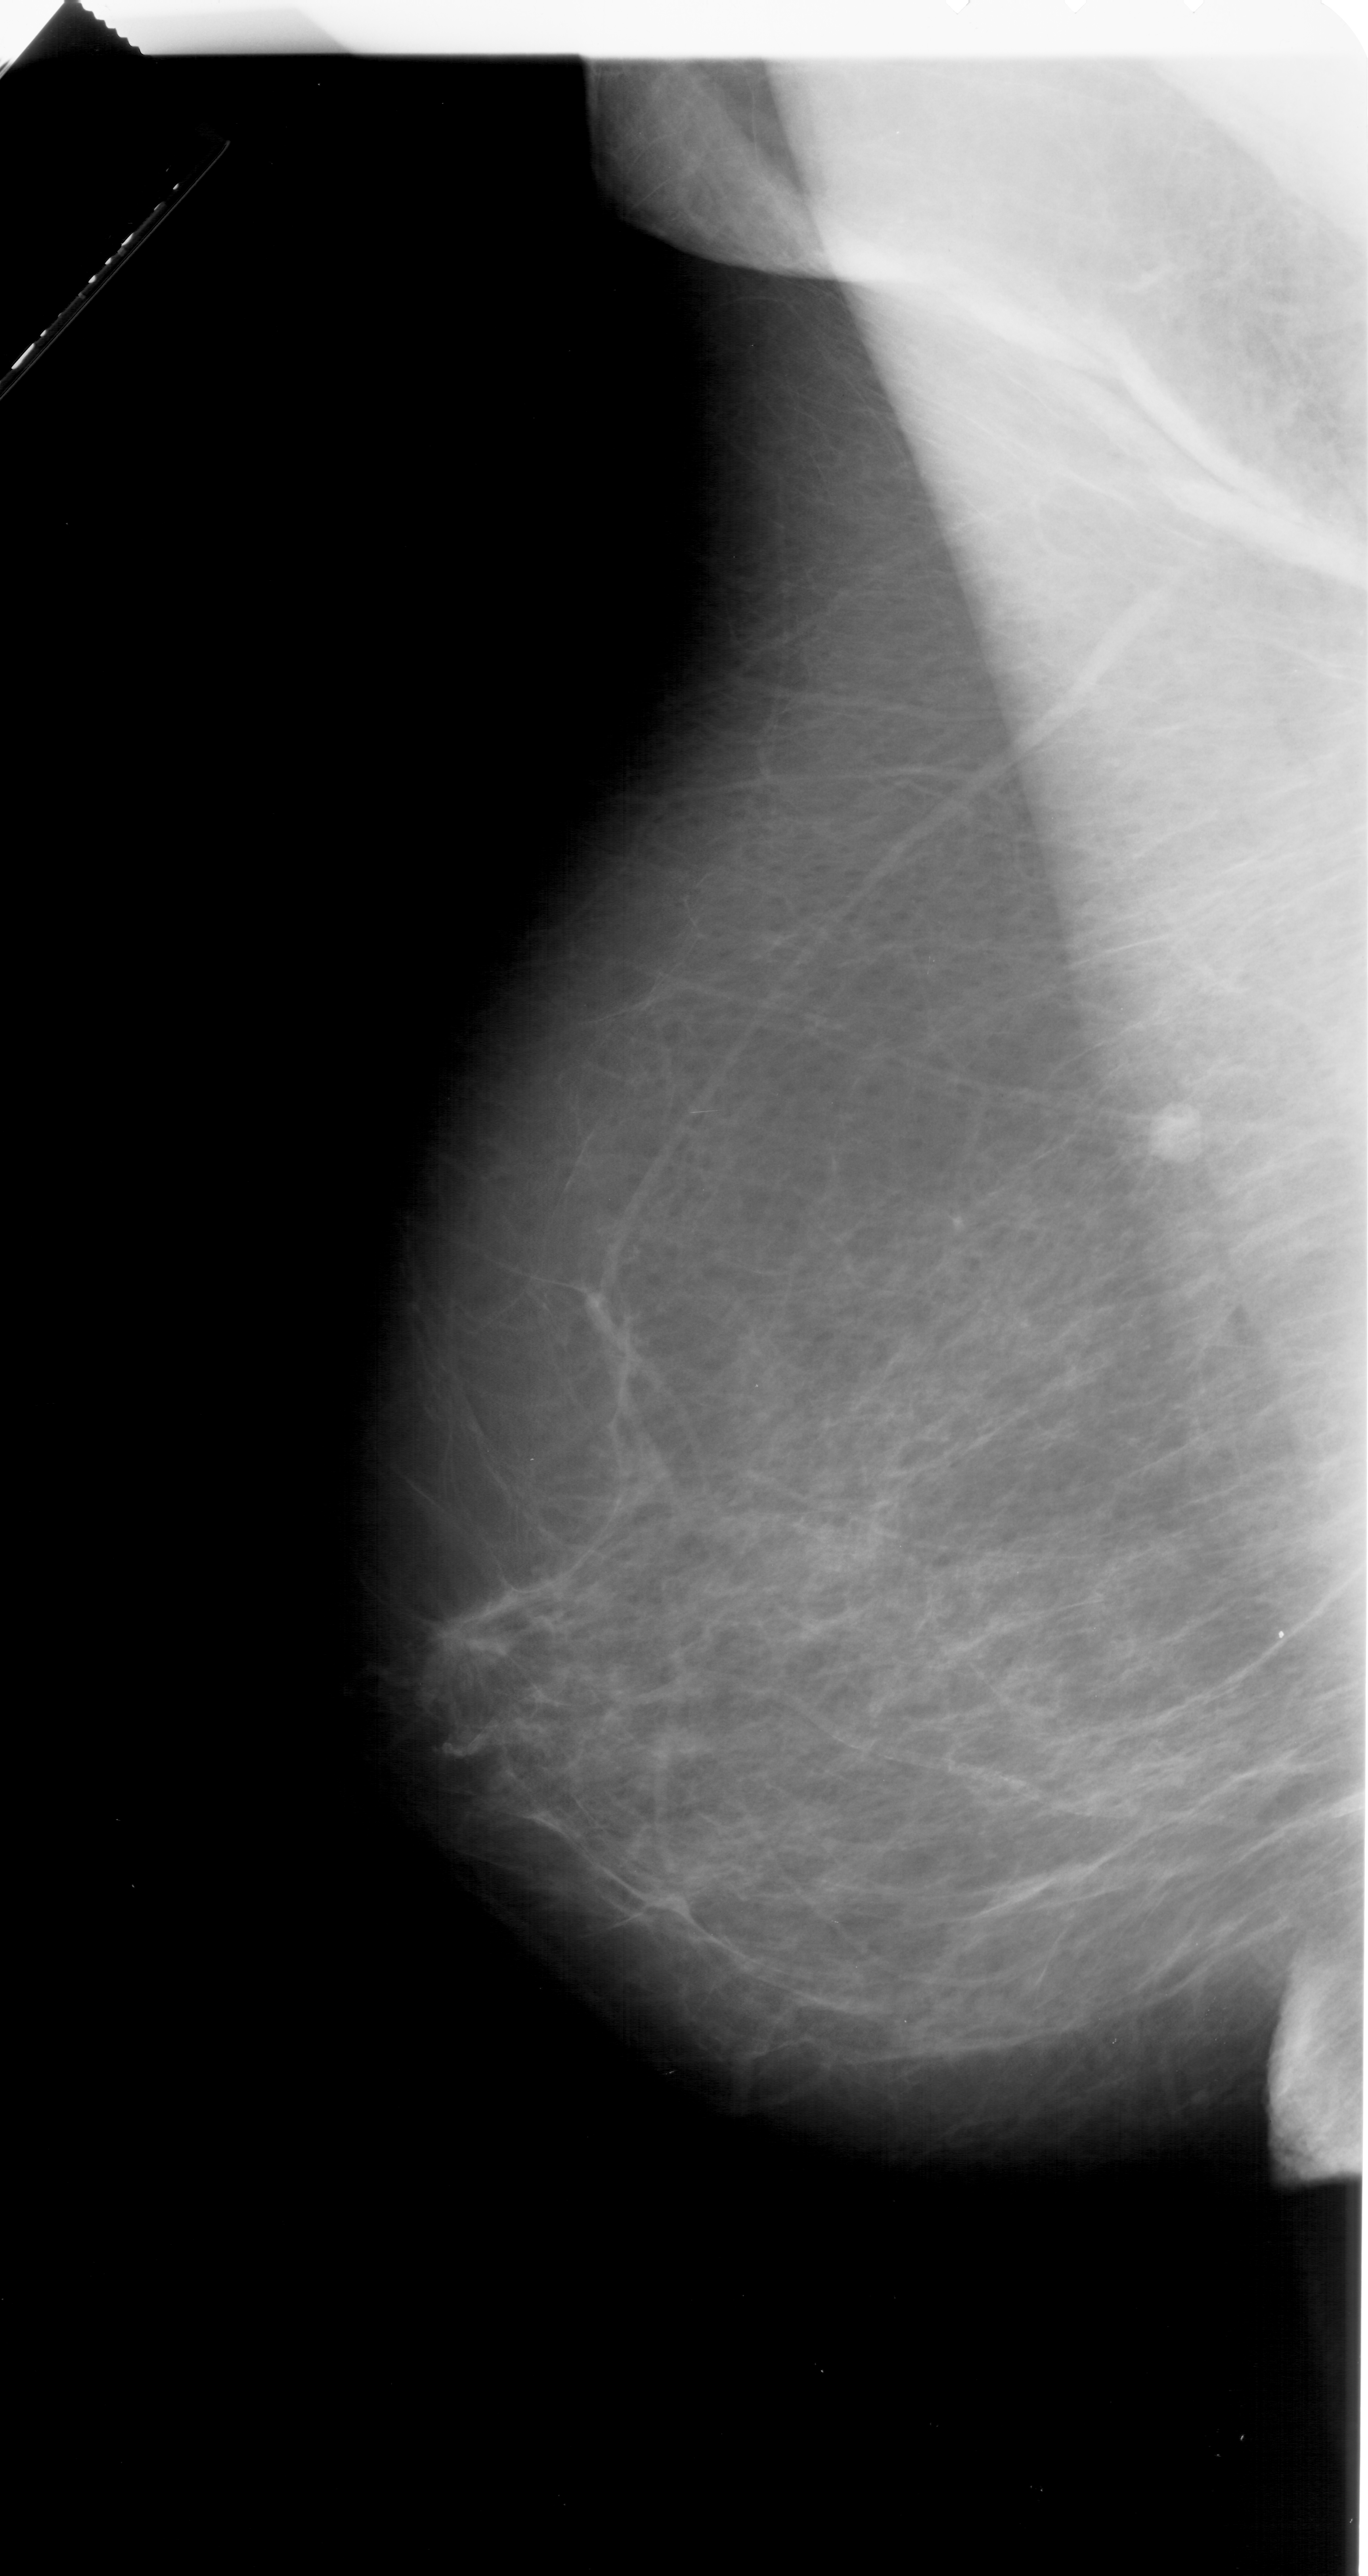
Mammogram (digitized film). Left breast. Mediolateral oblique (MLO) view. 1368 × 2576 image matrix.
Marked abnormalities (boxes around the expert regions of interest):
- mass, shape irregular, margins spiculated; BI-RADS assessment category 5; subtlety rating 1 on a 1 (subtle) to 5 (obvious) scale; pathology (as recorded): malignant: bounding box <428,1585,531,1689> (left, top, right, bottom; pixels)